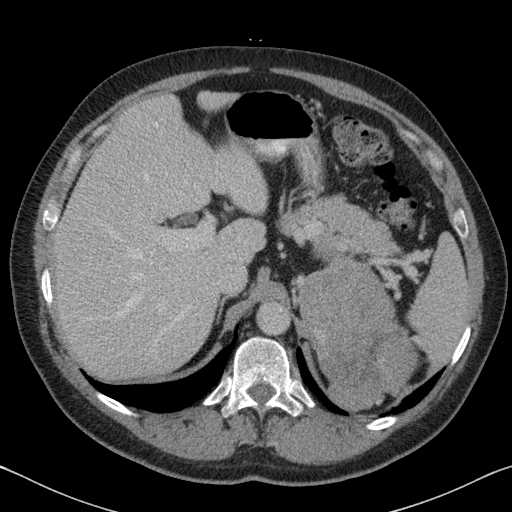
Contrast-enhanced abdominal CT, one axial slice. Reconstruction kernel B31f. Intravenous contrast given. Soft-tissue window (W 400 / L 40 HU). 3 mm slice thickness. 512 × 512 image matrix, field of view 366 × 366 mm. Patient: male, 51 years. From the clinical record (not read from this slice): diagnosis: adrenocortical carcinoma; tumour side: left adrenal; tumour size at pathology: 16.5 cm; Ki-67 index: 30 %; stage (as recorded): 2.
Annotated regions visible in this slice (semi-automatically segmented with operator editing):
- mass: box from (x=305, y=258) to (x=414, y=410) px